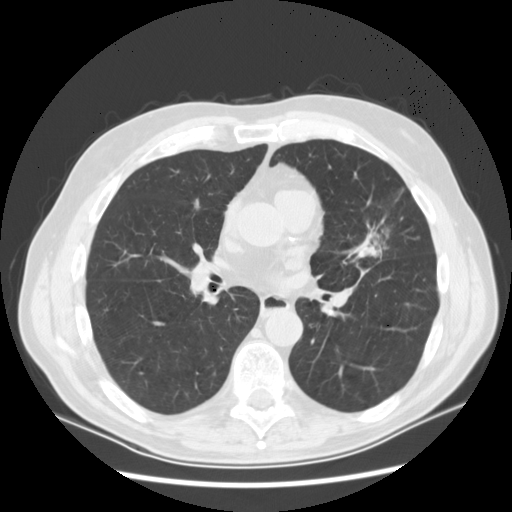
Axial slice from a low-dose chest CT screening exam; baseline annual screen; lung window (W 1500 / L -600 HU); standard (soft-tissue) reconstruction kernel (STANDARD); slice 65 of 132 in the series. Male, age 65 years at enrolment. Current smoker at enrolment.
Expert reader's lesion annotation, bounding box (x1, y1, x2, y2) in pixels: (346, 198, 415, 270). The exam's reader record, not a measurement of the box and not confirmed to be the same lesion: non-calcified nodule or mass ≥4 mm, left upper lobe, 37 × 27 mm, spiculated (stellate) margins, soft tissue attenuation. Participant outcome: lung cancer diagnosed 56 days after this screen — non-small cell carcinoma, poorly differentiated (G3), stage IA (AJCC 6th edition).